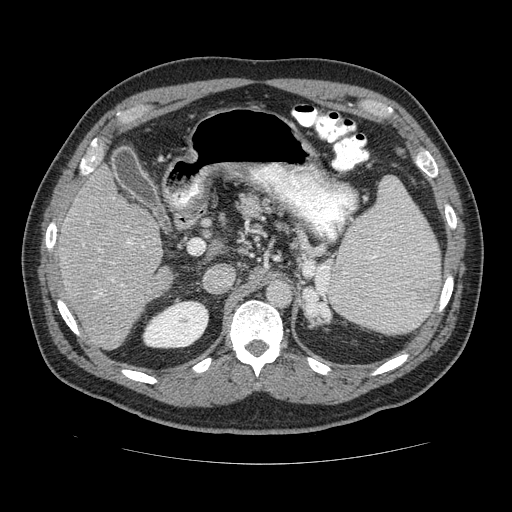
Contrast-enhanced abdominal CT (liver protocol), one axial slice. Position 76 of 113 along the scan axis. Reconstruction kernel STANDARD. 120 kVp. Soft-tissue window (W 400 / L 40 HU). 2.5 mm slice thickness. 512 × 512 image matrix, field of view 400 × 400 mm. Case-level facts recorded for this patient, not image findings: diagnosis: hepatocellular carcinoma (patient treated with transarterial chemoembolisation; whether this scan precedes or follows treatment is not stated here); TNM stage (as recorded): Stage-II; Child-Pugh class: B; tumour differentiation: moderately differentiated; tumour size: 4.8 cm.
Structures marked on this image (semi-automatically segmented with operator editing):
- liver parenchyma outside the tumour (the mass and vessels are separate outlines, so this box may not span the whole liver): bounding box <52,164,179,350> (left, top, right, bottom; pixels)
- liver vessels: <99,241,135,294>